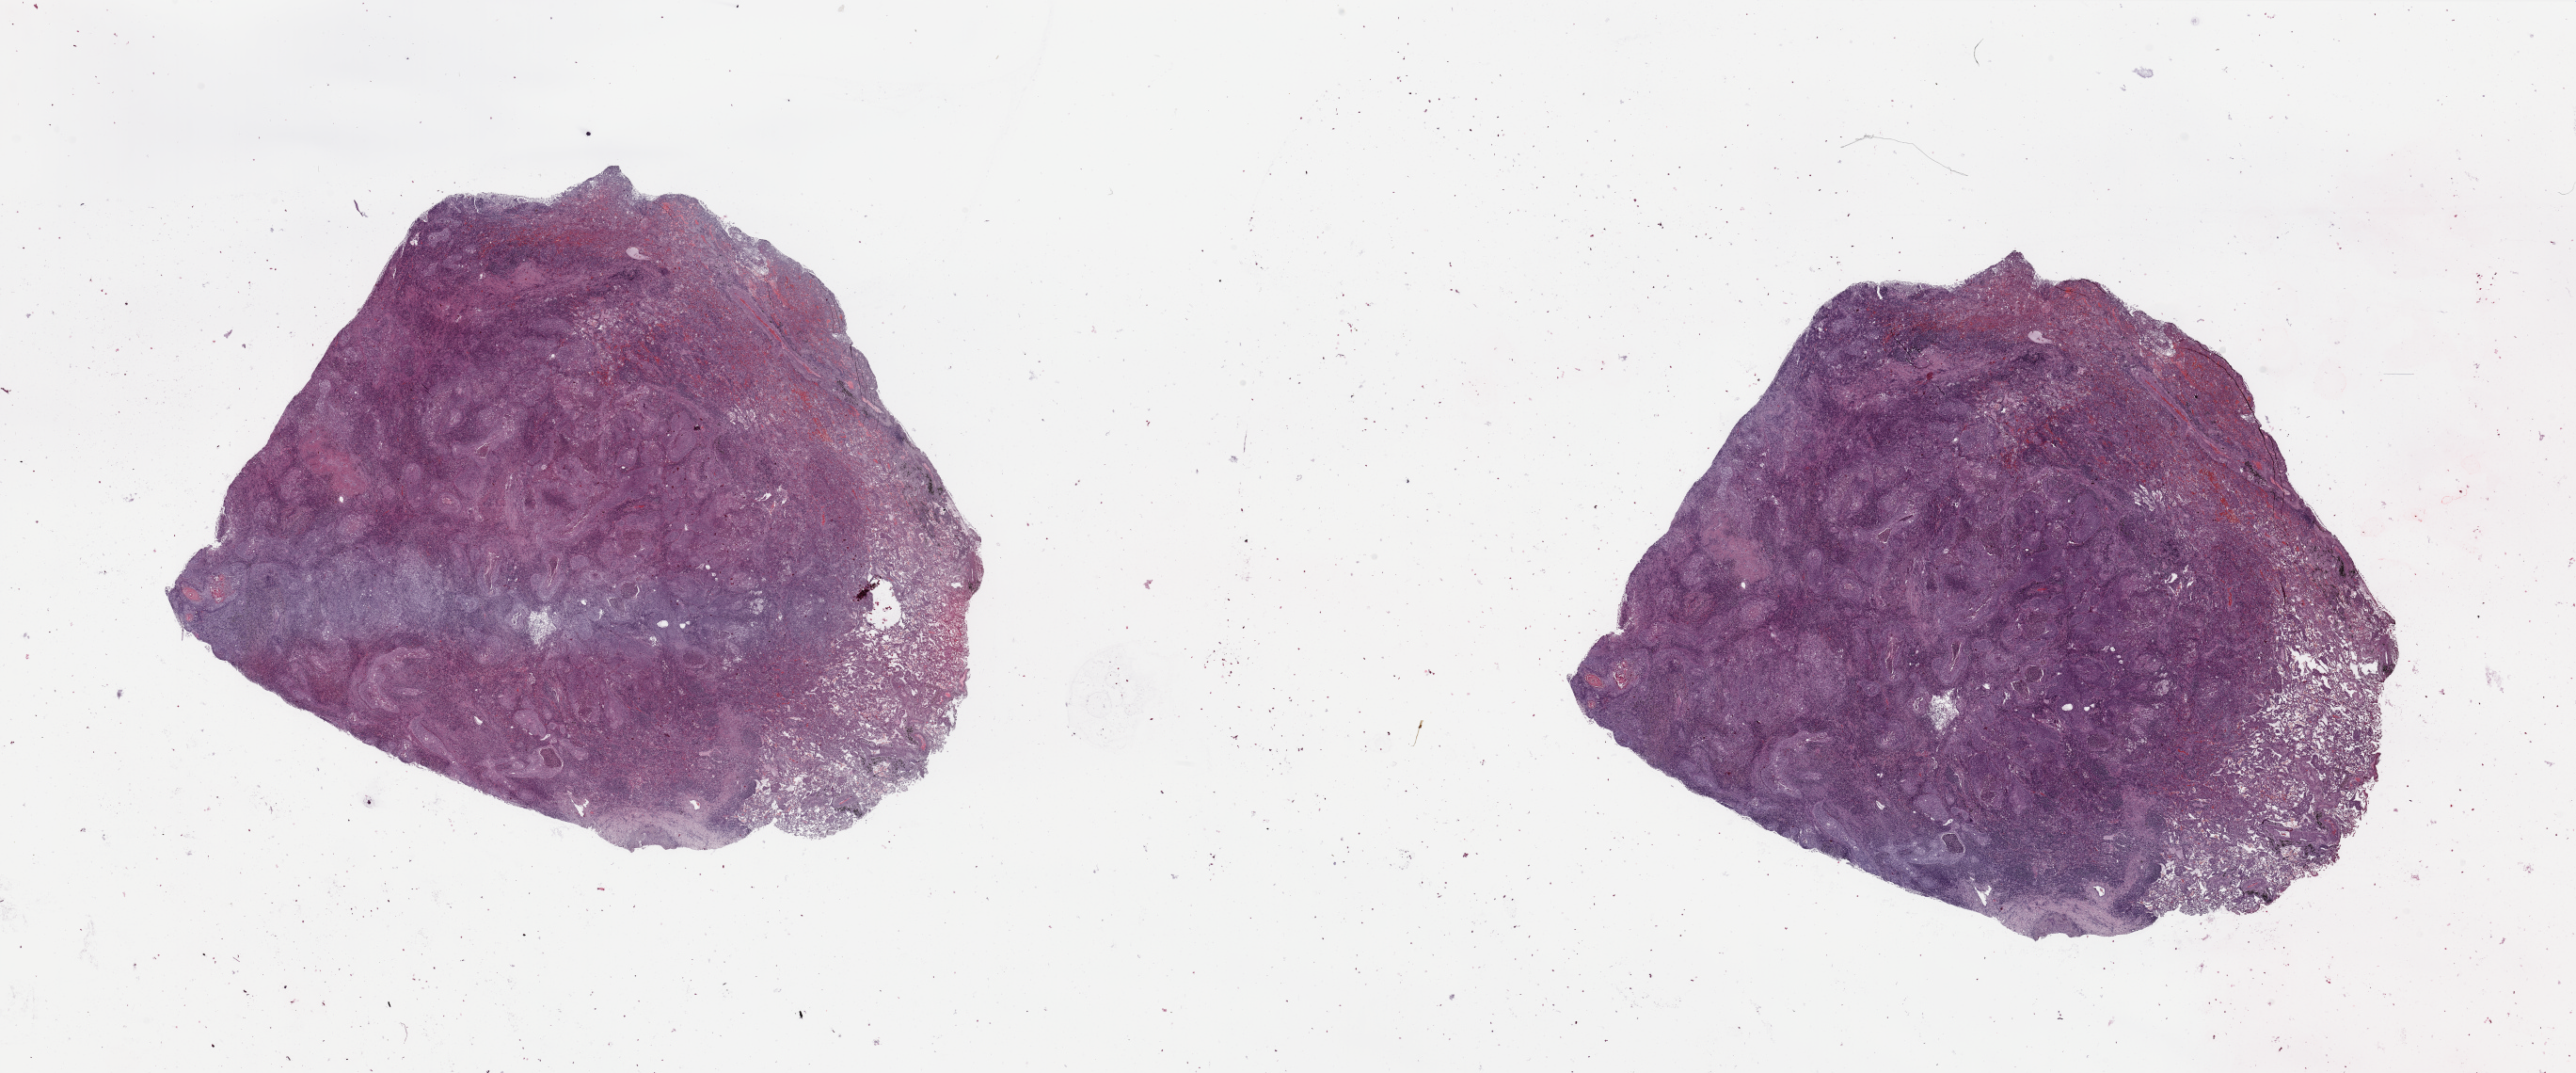
Whole-slide histology image, H&E — shown as a low-resolution overview of the whole scanned area (about 43.3 x 18.0 mm, slide scanned at 20x), lung, tumour tissue. Male, 70 y/o. Histologic grade: G2 (moderately differentiated).
Primary tumour site (as recorded): left lower lobe. Histologic diagnosis: Squamous cell carcinoma, NOS. AJCC pathologic stage: IB.